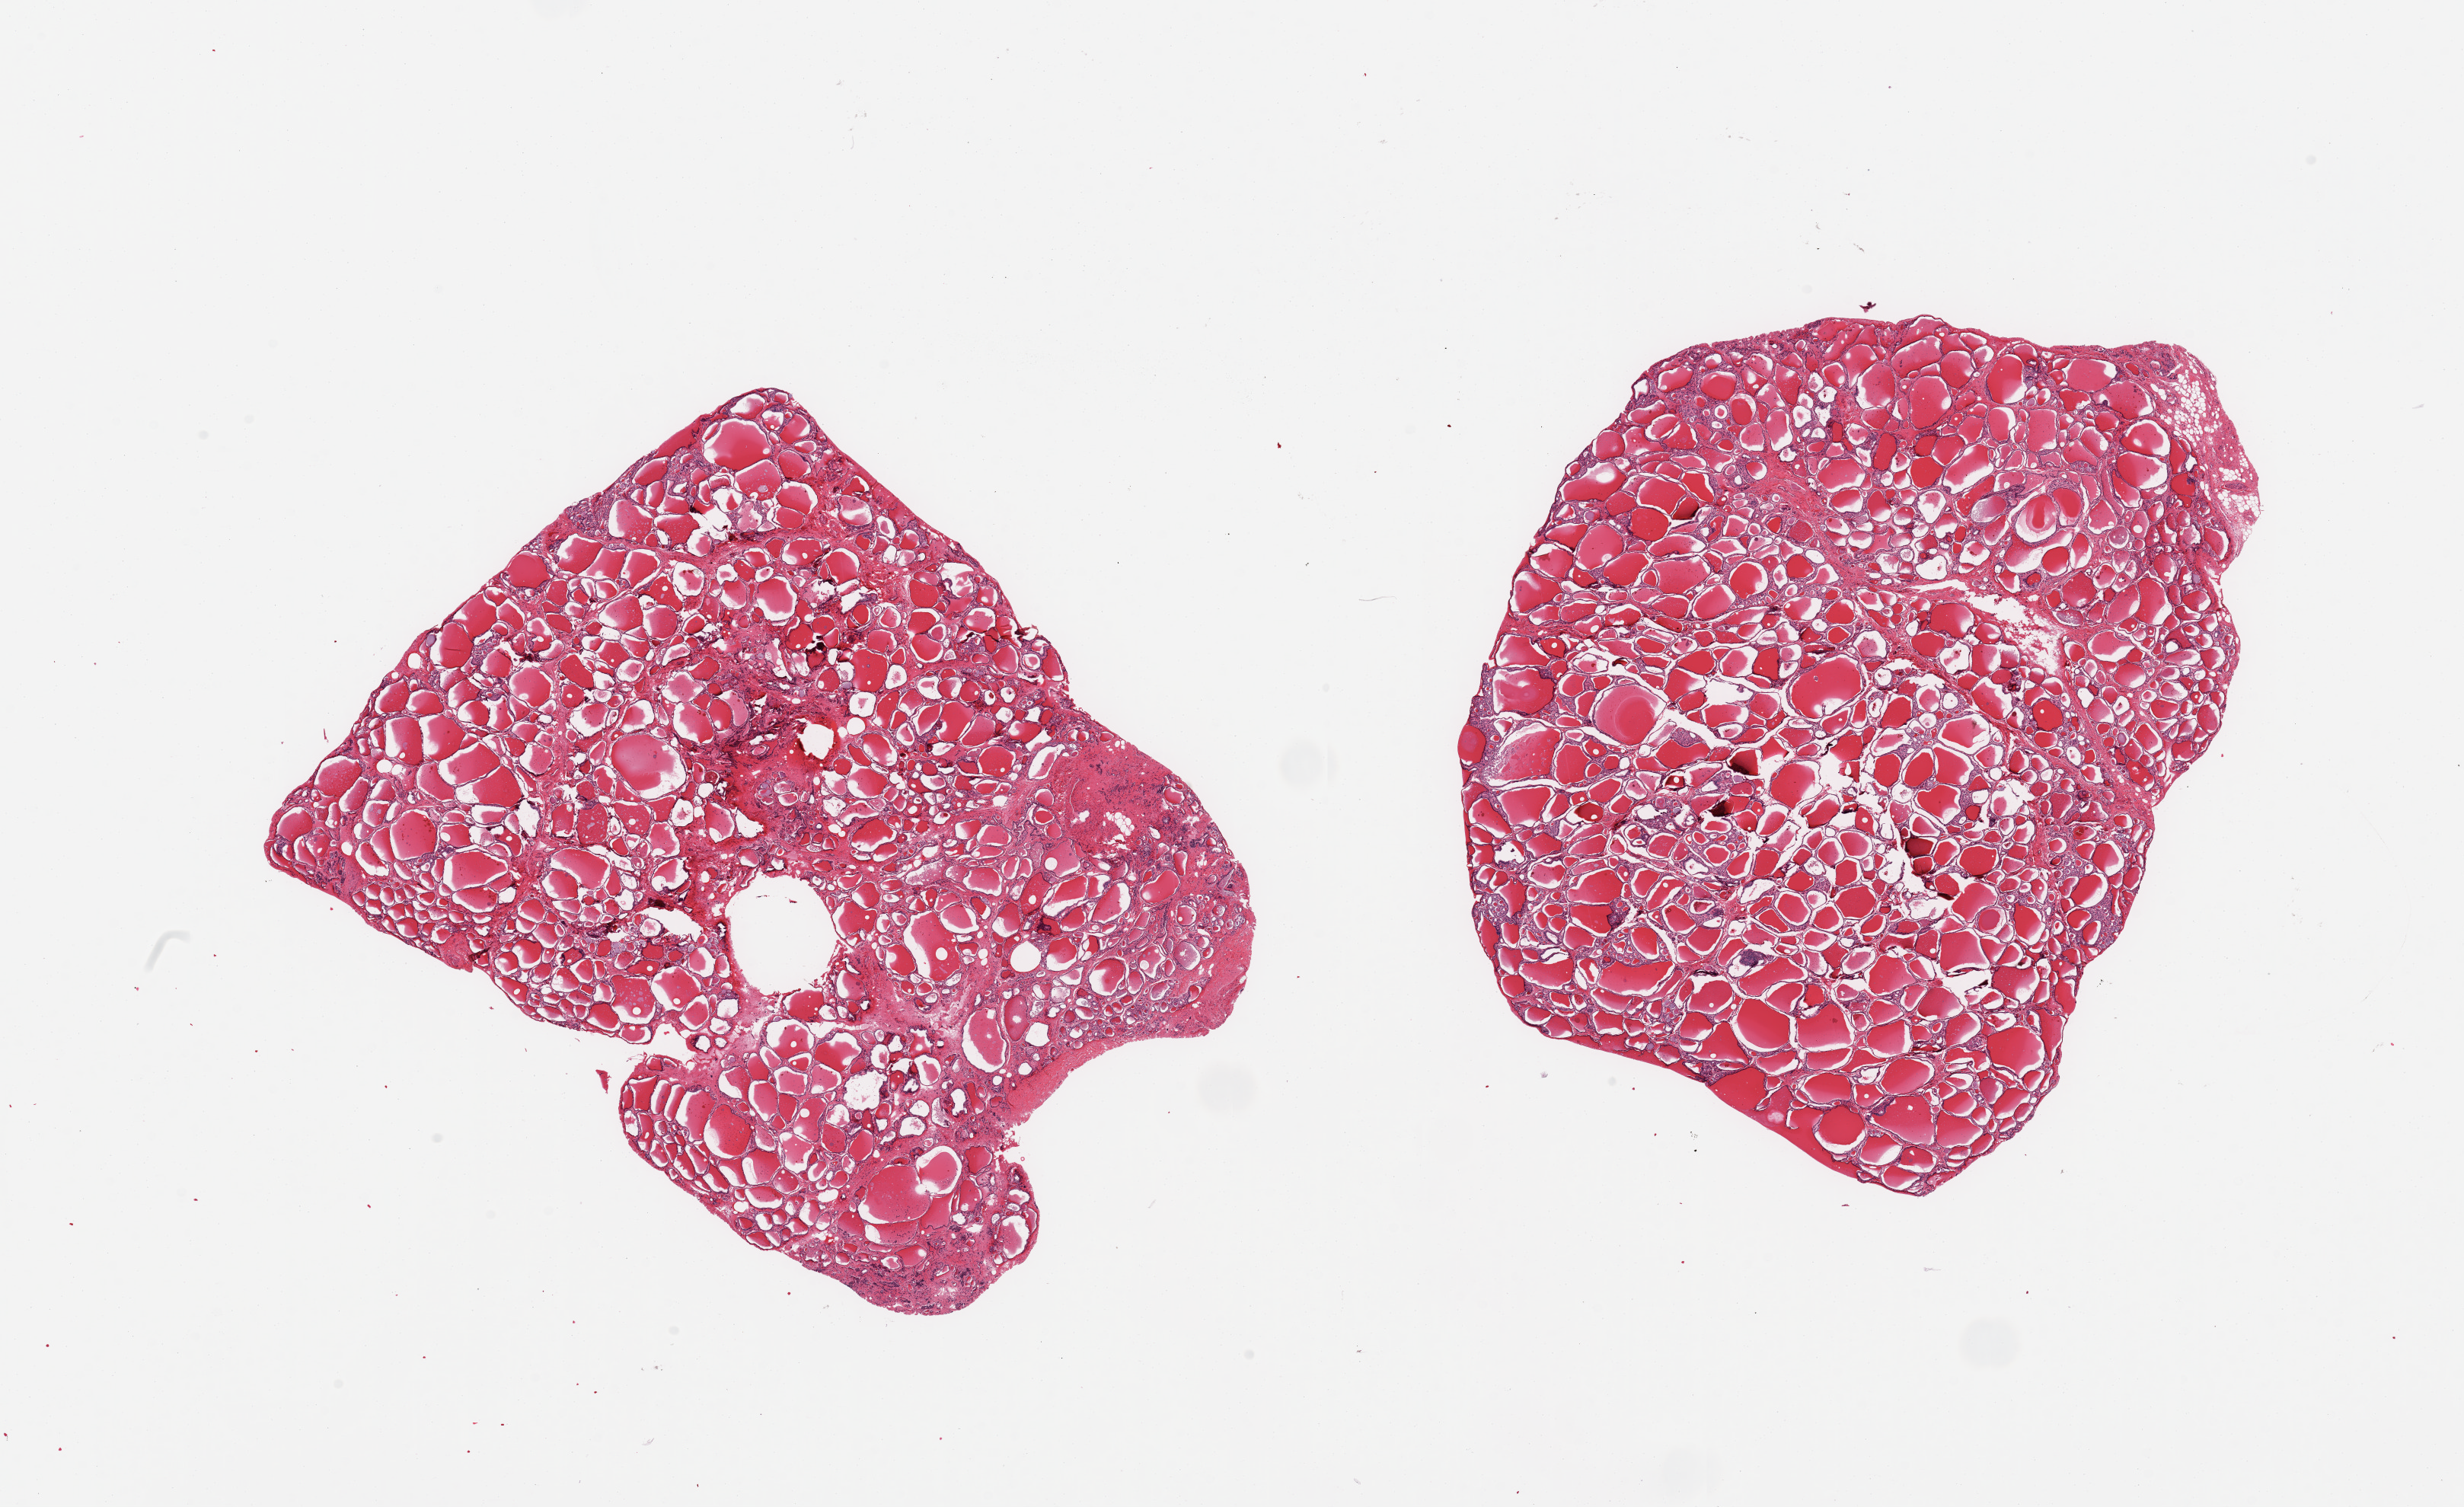
H&E whole-slide image, shown as a low-resolution overview of the whole scanned area (about 25.6 x 15.7 mm, slide scanned at 20x). PAXgene-fixed paraffin-embedded (PFPE) section. Target tissue: thyroid. Tissue donor sample. Male donor.
Reviewer comment on this tissue sample: 2 pieces; variably sized follicles with some fibrosis and degenerative change.